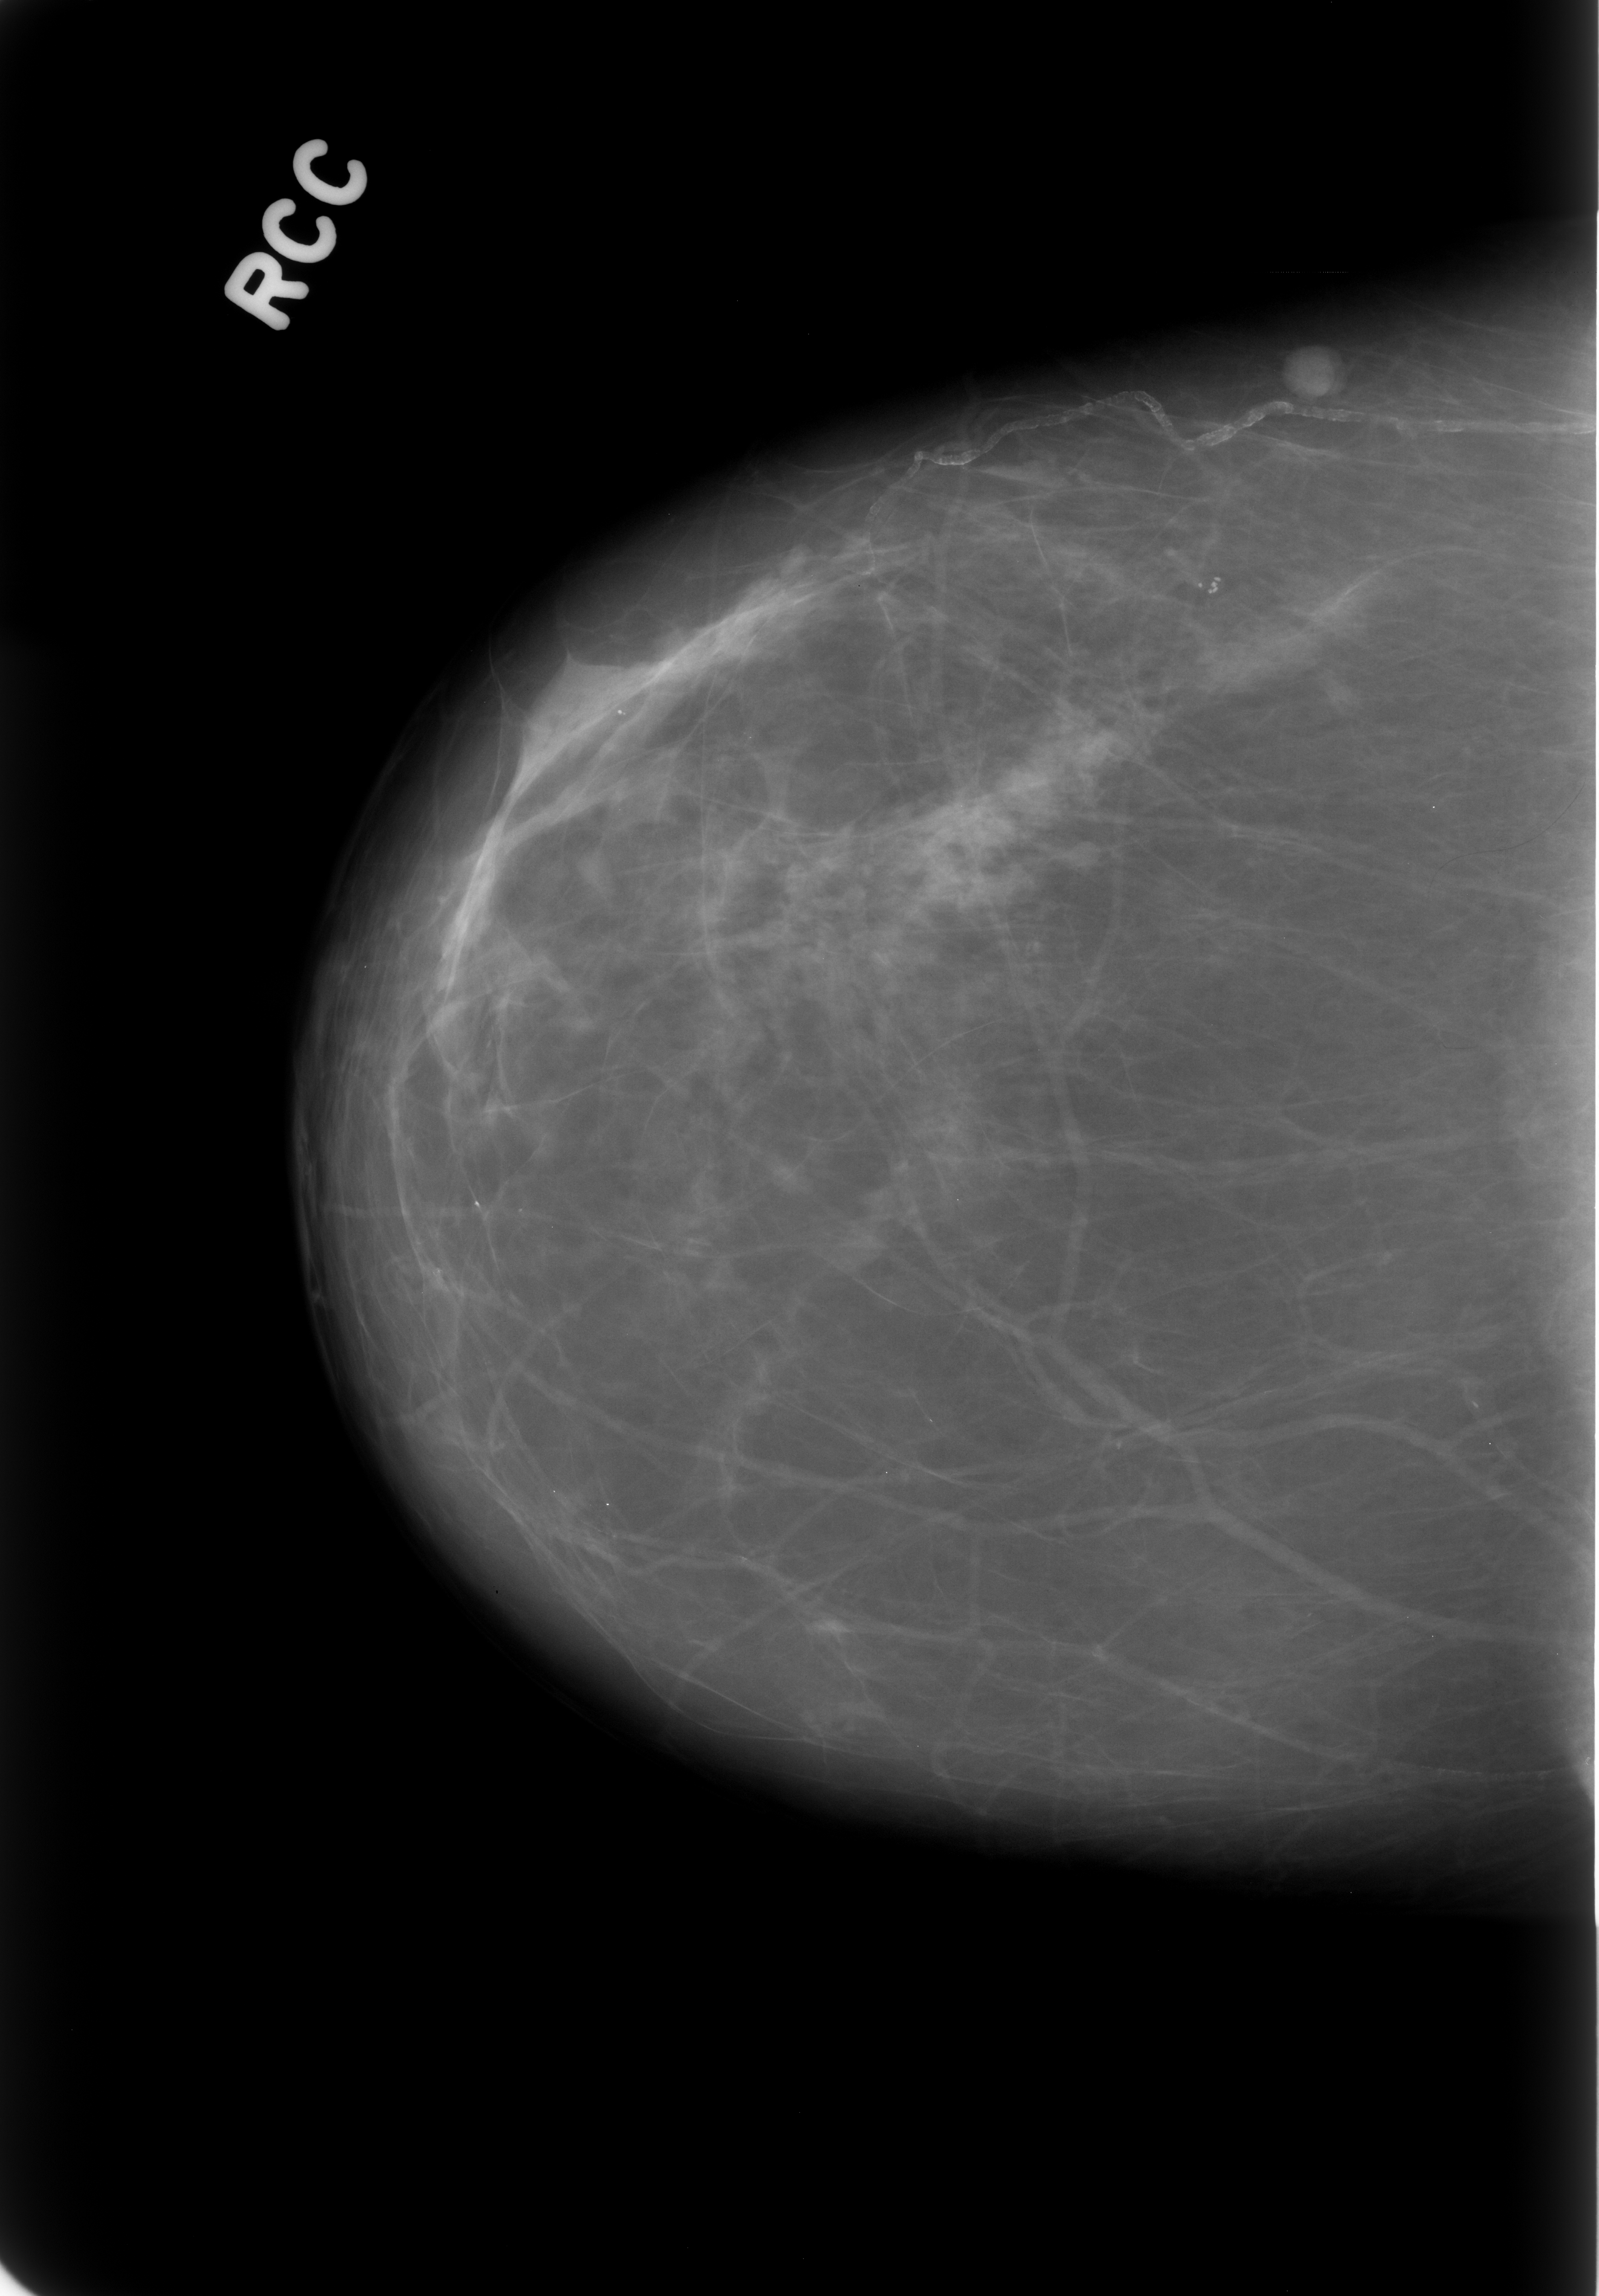
Scanned film-screen mammogram; right breast; craniocaudal (CC) view; BI-RADS breast density category 1 (scale 1–4); 1599 × 2296 image matrix.
Expert-marked regions of interest on this film, with their recorded descriptors:
- mass, shape round, margins circumscribed; BI-RADS assessment category 3; subtlety rating 5 on a 1 (subtle) to 5 (obvious) scale; pathology (as recorded): benign: bounding box [x1, y1, x2, y2] px = [1275, 335, 1354, 411]